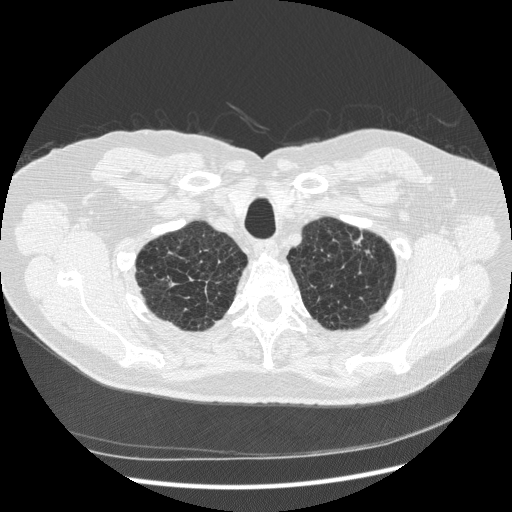
Axial slice from a low-dose chest CT screening exam. Baseline screening round. Lung window (W 1500 / L -600 HU). 1.25 mm slice thickness. Standard (soft-tissue) reconstruction kernel (STANDARD). 512 × 512 image matrix, field of view 380 × 380 mm. Male participant, aged 70 years at enrolment. Former smoker at enrolment.
Expert-annotated lung lesion, bounding box [x1, y1, x2, y2] px = [333, 222, 389, 278]. The screening reader recorded 2 non-calcified nodules or masses ≥4 mm on this exam; which of them this box marks is not recorded. Participant outcome: lung cancer diagnosed 816 days after this screen — squamous cell carcinoma, NOS, left upper lobe, moderately differentiated (G2), stage IA (AJCC 6th edition), 18 mm at pathology.